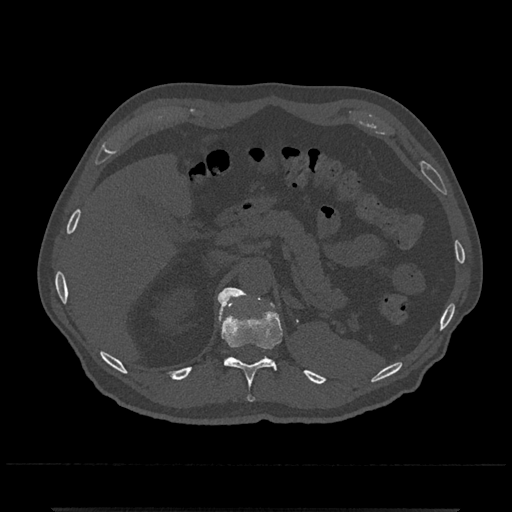
CT including the spine, one axial slice. Slice 478 of 797 in the series (ordered by position). Bone window (W 1800 / L 400 HU). 0.5 mm slice thickness. 512 × 512 image matrix. Male patient, age 67 years. From the clinical record (not read from this slice): primary cancer: prostate.
Structures marked on this image (semi-automatic segmentation, software-assisted and operator-edited):
- T11 vertebra: box from (x=218, y=295) to (x=282, y=402) px
- T12 vertebra: (x=219, y=287)–(x=248, y=307)